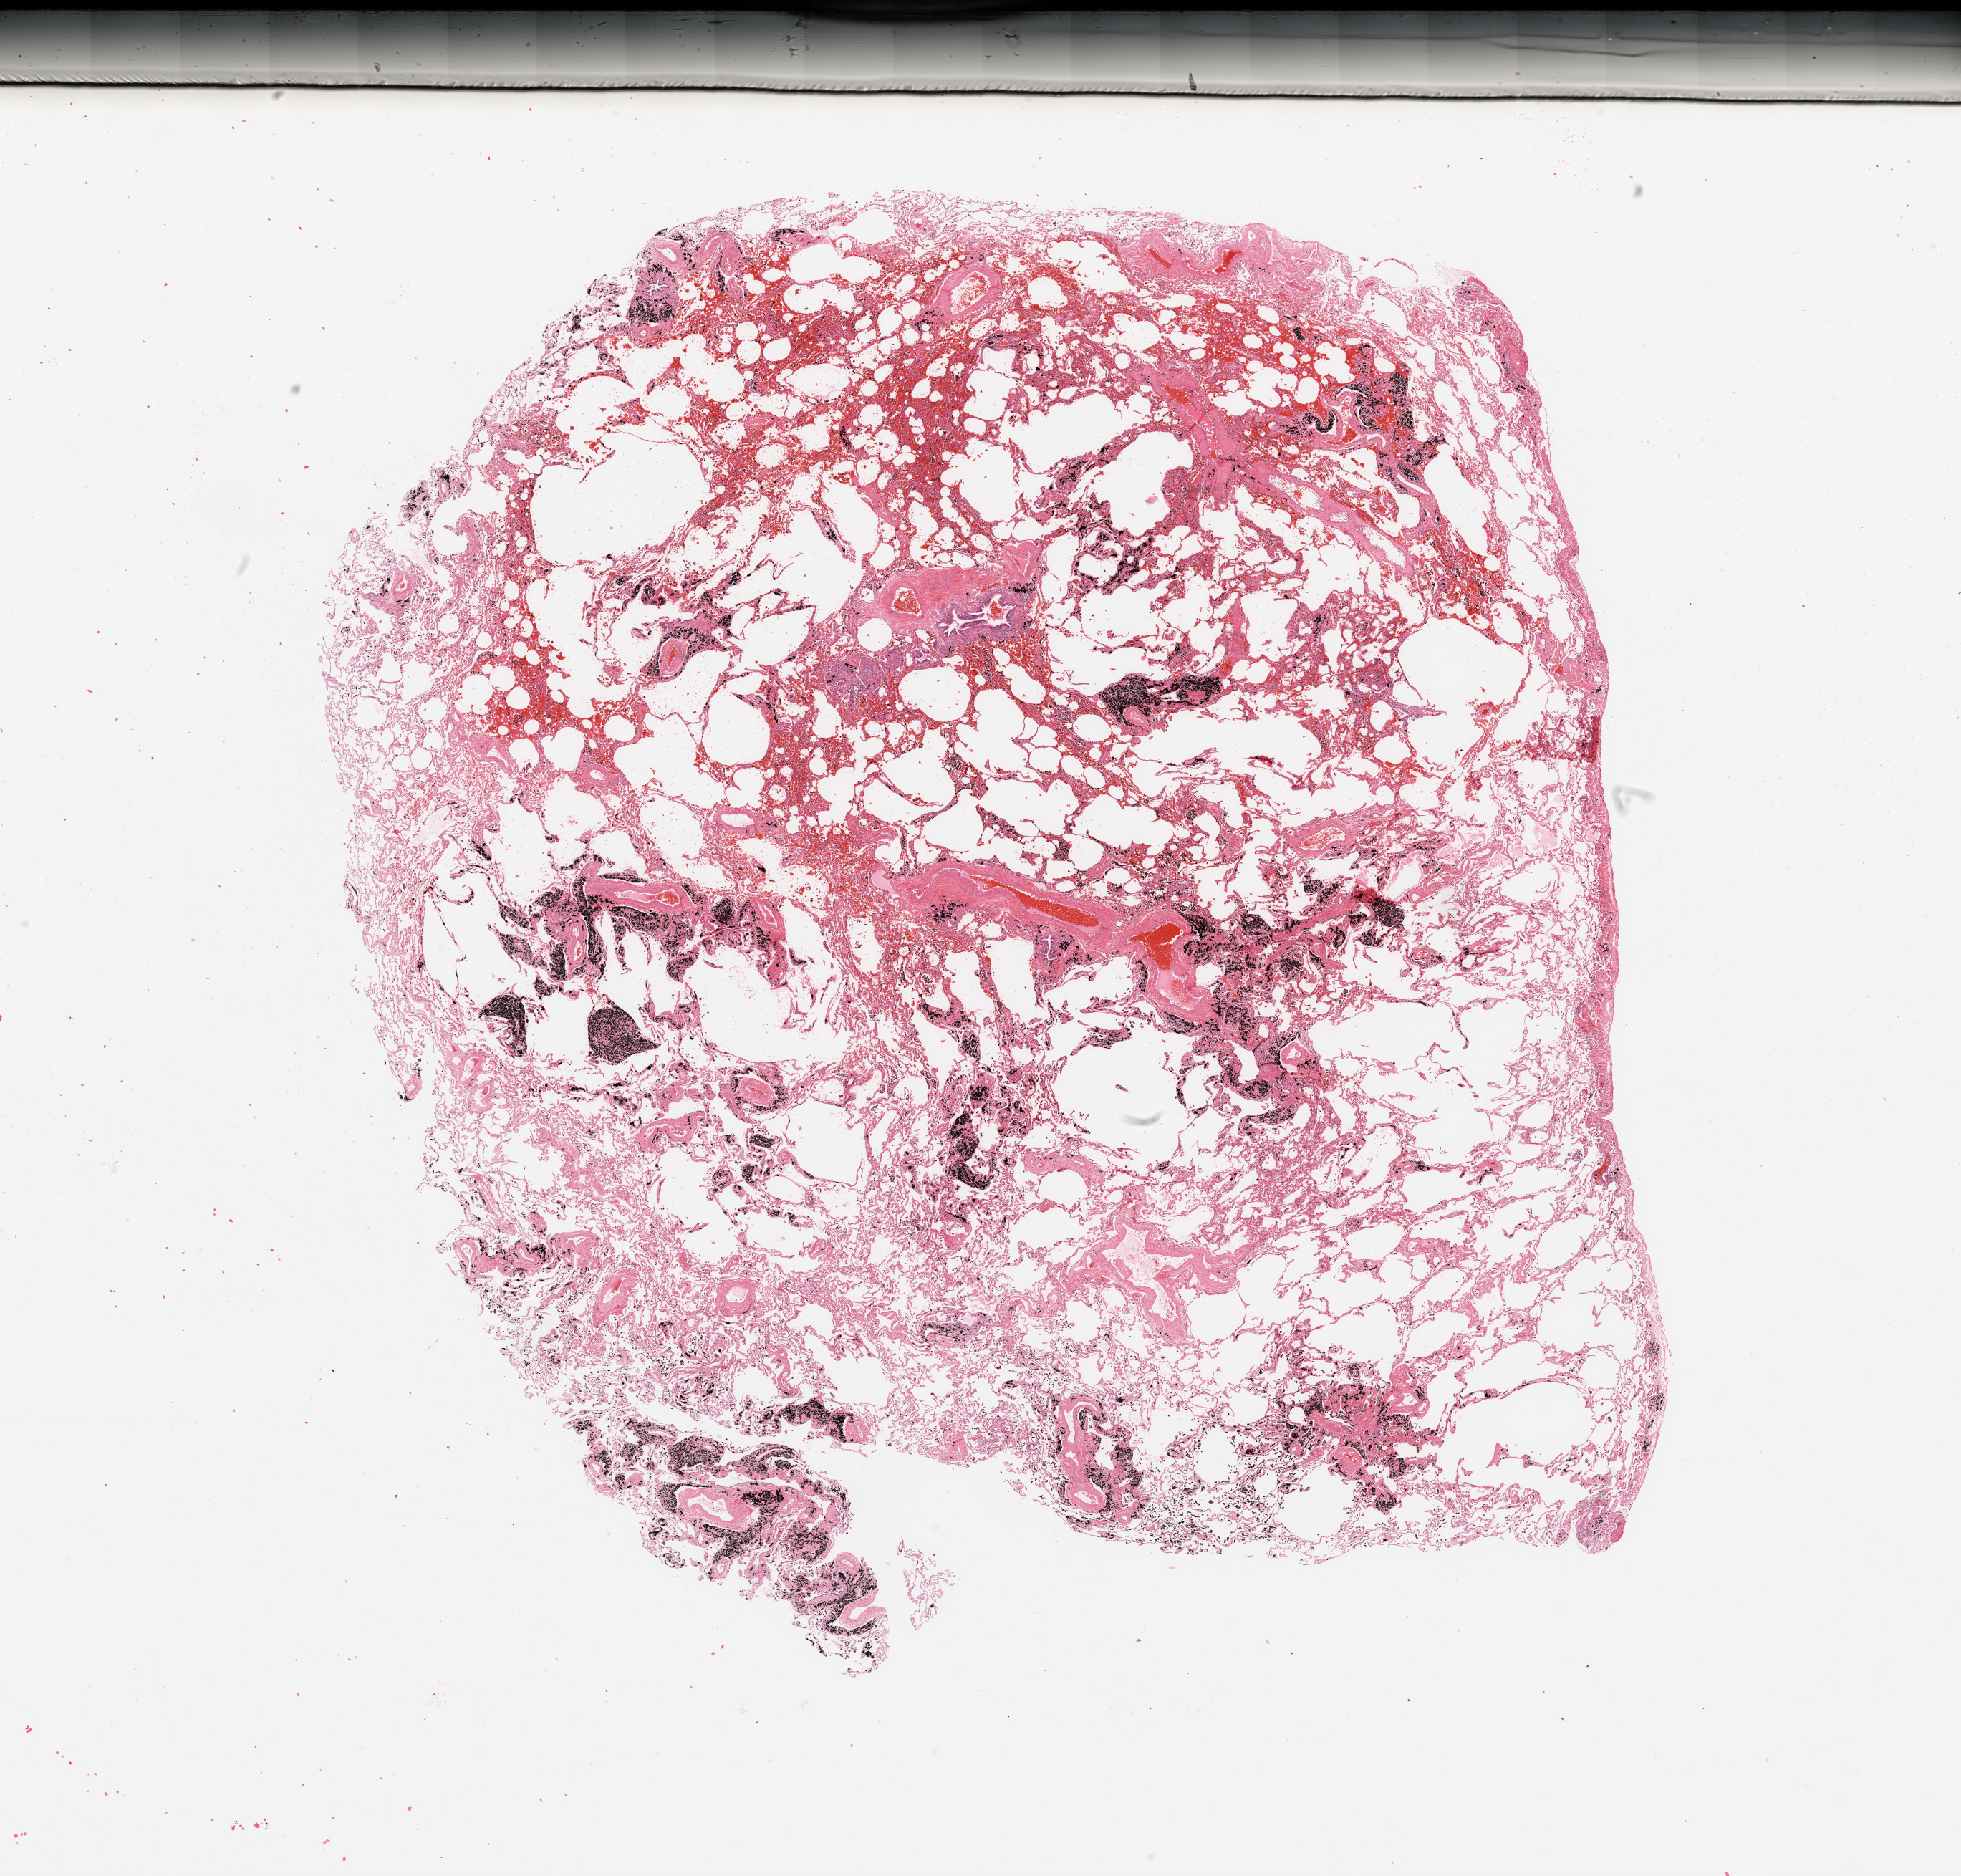
Whole-slide histology image, Hematoxylin and eosin (H&E) stained, whole scanned area (about 21.7 x 20.7 mm) shown as a low-resolution overview, normal (non-tumour) tissue sample, sampled site: lung. Male, 56 y/o.
• this section: normal (non-tumour) tissue from the same patient
• patient diagnosis: Squamous cell carcinoma, NOS